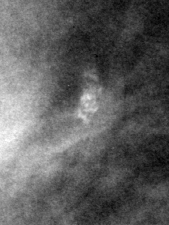
Crop from a digitized film mammogram around one marked abnormality; right breast; MLO view.
Finding: calcifications, morphology pleomorphic, distribution clustered; BI-RADS assessment category 4; pathology result (as recorded, not read from the image): benign.